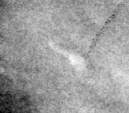
Region of interest cut from a scanned film mammogram (one marked finding); left breast; MLO view.
Marked abnormality: calcifications, morphology round and regular / lucent centered; BI-RADS assessment category 2; benign; no additional work-up was recommended (benign without callback).